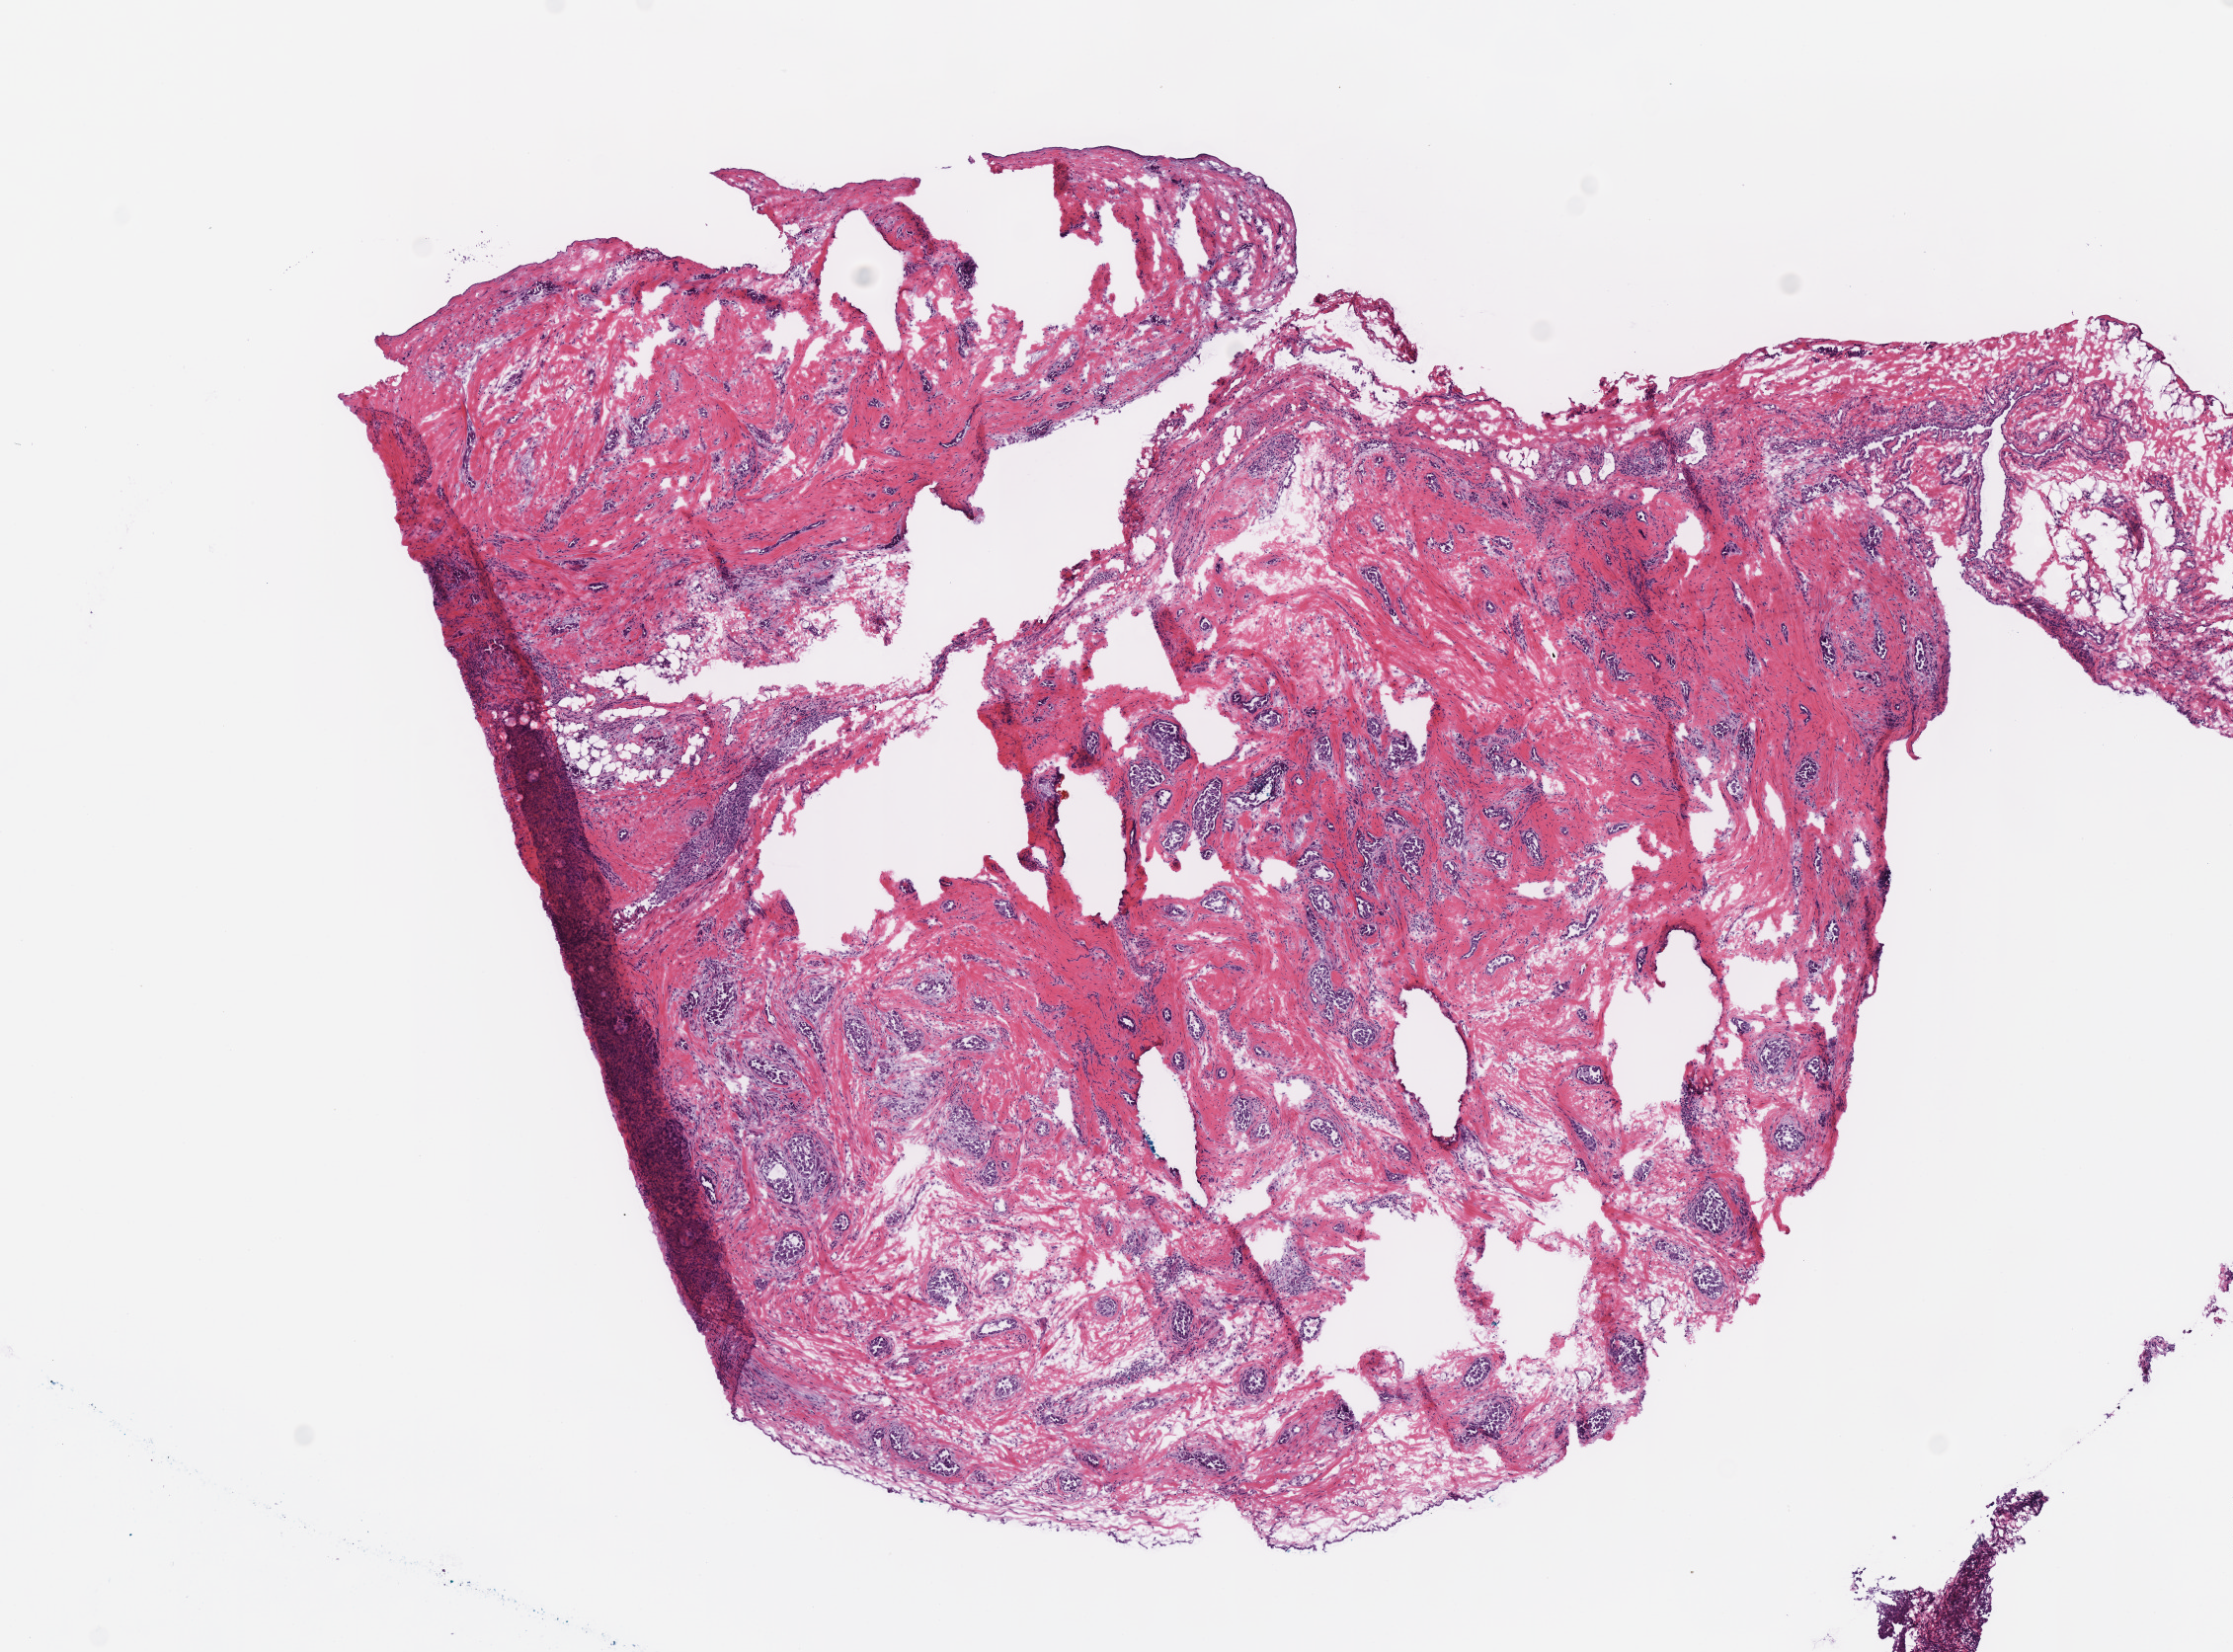
Hematoxylin and eosin (H&E) stained whole-slide image, a low-resolution overview of the entire scanned area, about 8.9 x 6.6 mm; frozen section from the top of the tissue portion; lung, primary tumour sample. Female patient; age at initial diagnosis 49 years. Pathologist review of this section (percent, as recorded): tumour cells 90%, tumour nuclei 70%, normal cells 0%, stromal cells 10%, necrosis 0%. Inflammatory infiltration, as recorded: lymphocyte infiltration 10%.
Diagnosis: Adenocarcinoma, NOS. AJCC pathologic stage: IV (7th edition).